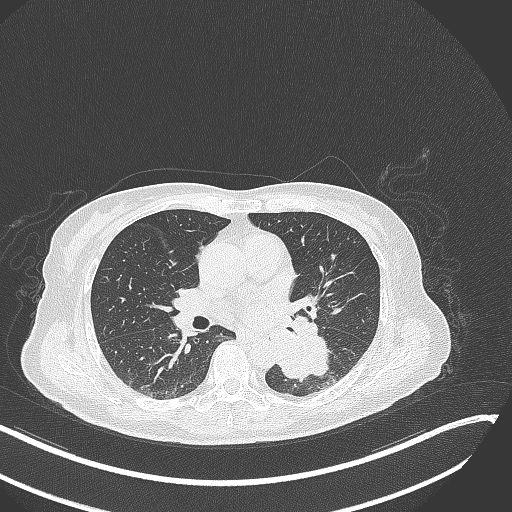
Chest CT, one axial slice; slice 144 of 342 in the series (ordered by position); reconstruction kernel B70f; 120 kVp; lung window (W 1500 / L -600 HU); 512 × 512 image matrix. Patient: female, 64 years. From the clinical record (not read from this slice): clinical TNM (as recorded): T3 N1 M1.
Annotated regions visible in this slice (rectangle marked by the reading radiologist):
- lung tumour (recorded histology: small cell carcinoma): bounding box [x1, y1, x2, y2] px = [269, 324, 335, 384]